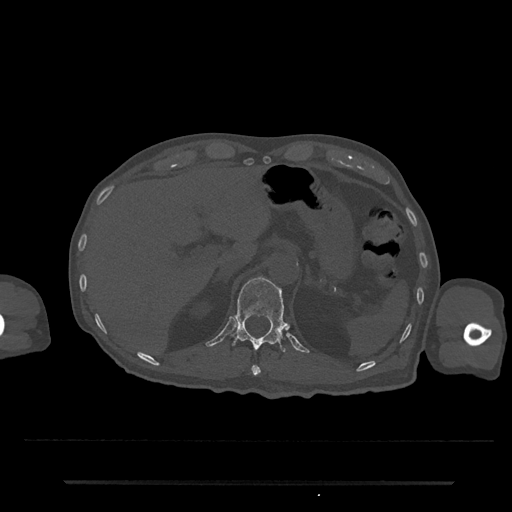
CT including the spine, one axial slice; position 198 of 797 along the scan axis; bone window (W 1800 / L 400 HU); 0.5 mm slice thickness; 512 × 512 image matrix, field of view 427 × 427 mm. Male patient, age 74 years. From the clinical record (not read from this slice): primary cancer: prostate.
Annotated regions visible in this slice (semi-automatically segmented with operator editing):
- T11 vertebra: box from (x=251, y=365) to (x=261, y=376) px
- T12 vertebra: (x=232, y=277)–(x=286, y=352)